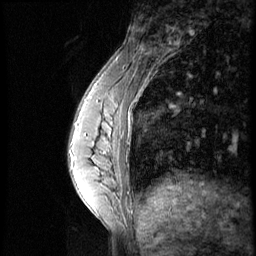
Breast MRI (dynamic contrast-enhanced), one sagittal slice; slice 16 of 56 in the series (ordered by position); dynamic contrast-enhanced series, image 2 of 4 at this slice position (ordered by acquisition); 1.5 T; TE 4.2 ms, TR 8.9 ms; 256 × 256 image matrix. Patient: female, 35 years. Case-level facts recorded for this patient, not image findings: setting: breast cancer imaged before/during neoadjuvant chemotherapy; receptor status: HER2-positive.
Structures marked on this image (semi-automatic segmentation, software-assisted and operator-edited):
- analysis volume of interest (the breast-tissue region the enhancement analysis was run in; not a lesion): bounding box (x1, y1, x2, y2) in pixels: (73, 111, 131, 164)
- tumour enhancement mask (voxels above the 140 % enhancement threshold inside the analysis volume of interest): (76, 113, 114, 153)